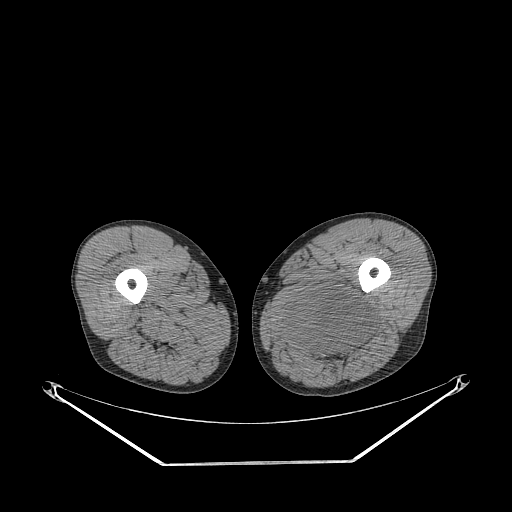
CT of an extremity soft-tissue mass (from a PET/CT study), one axial slice. Slice 248 of 267 in the series (ordered by position). Reconstruction kernel STANDARD. 140 kVp. Soft-tissue window (W 400 / L 40 HU). 3.75 mm slice thickness. 512 × 512 image matrix, field of view 500 × 500 mm. Male patient. From the clinical record (not read from this slice): histological type: undifferentiated pleomorphic liposarcoma; grade: high; site of the primary tumour: left thigh.
Outlined on this slice (expert contour drawn on MRI and transferred to this co-registered scan by the dataset authors):
- gross tumour volume including surrounding oedema: bounding box (x1, y1, x2, y2) in pixels: (279, 288, 375, 360)
- gross tumour volume (mass): (288, 288, 375, 352)